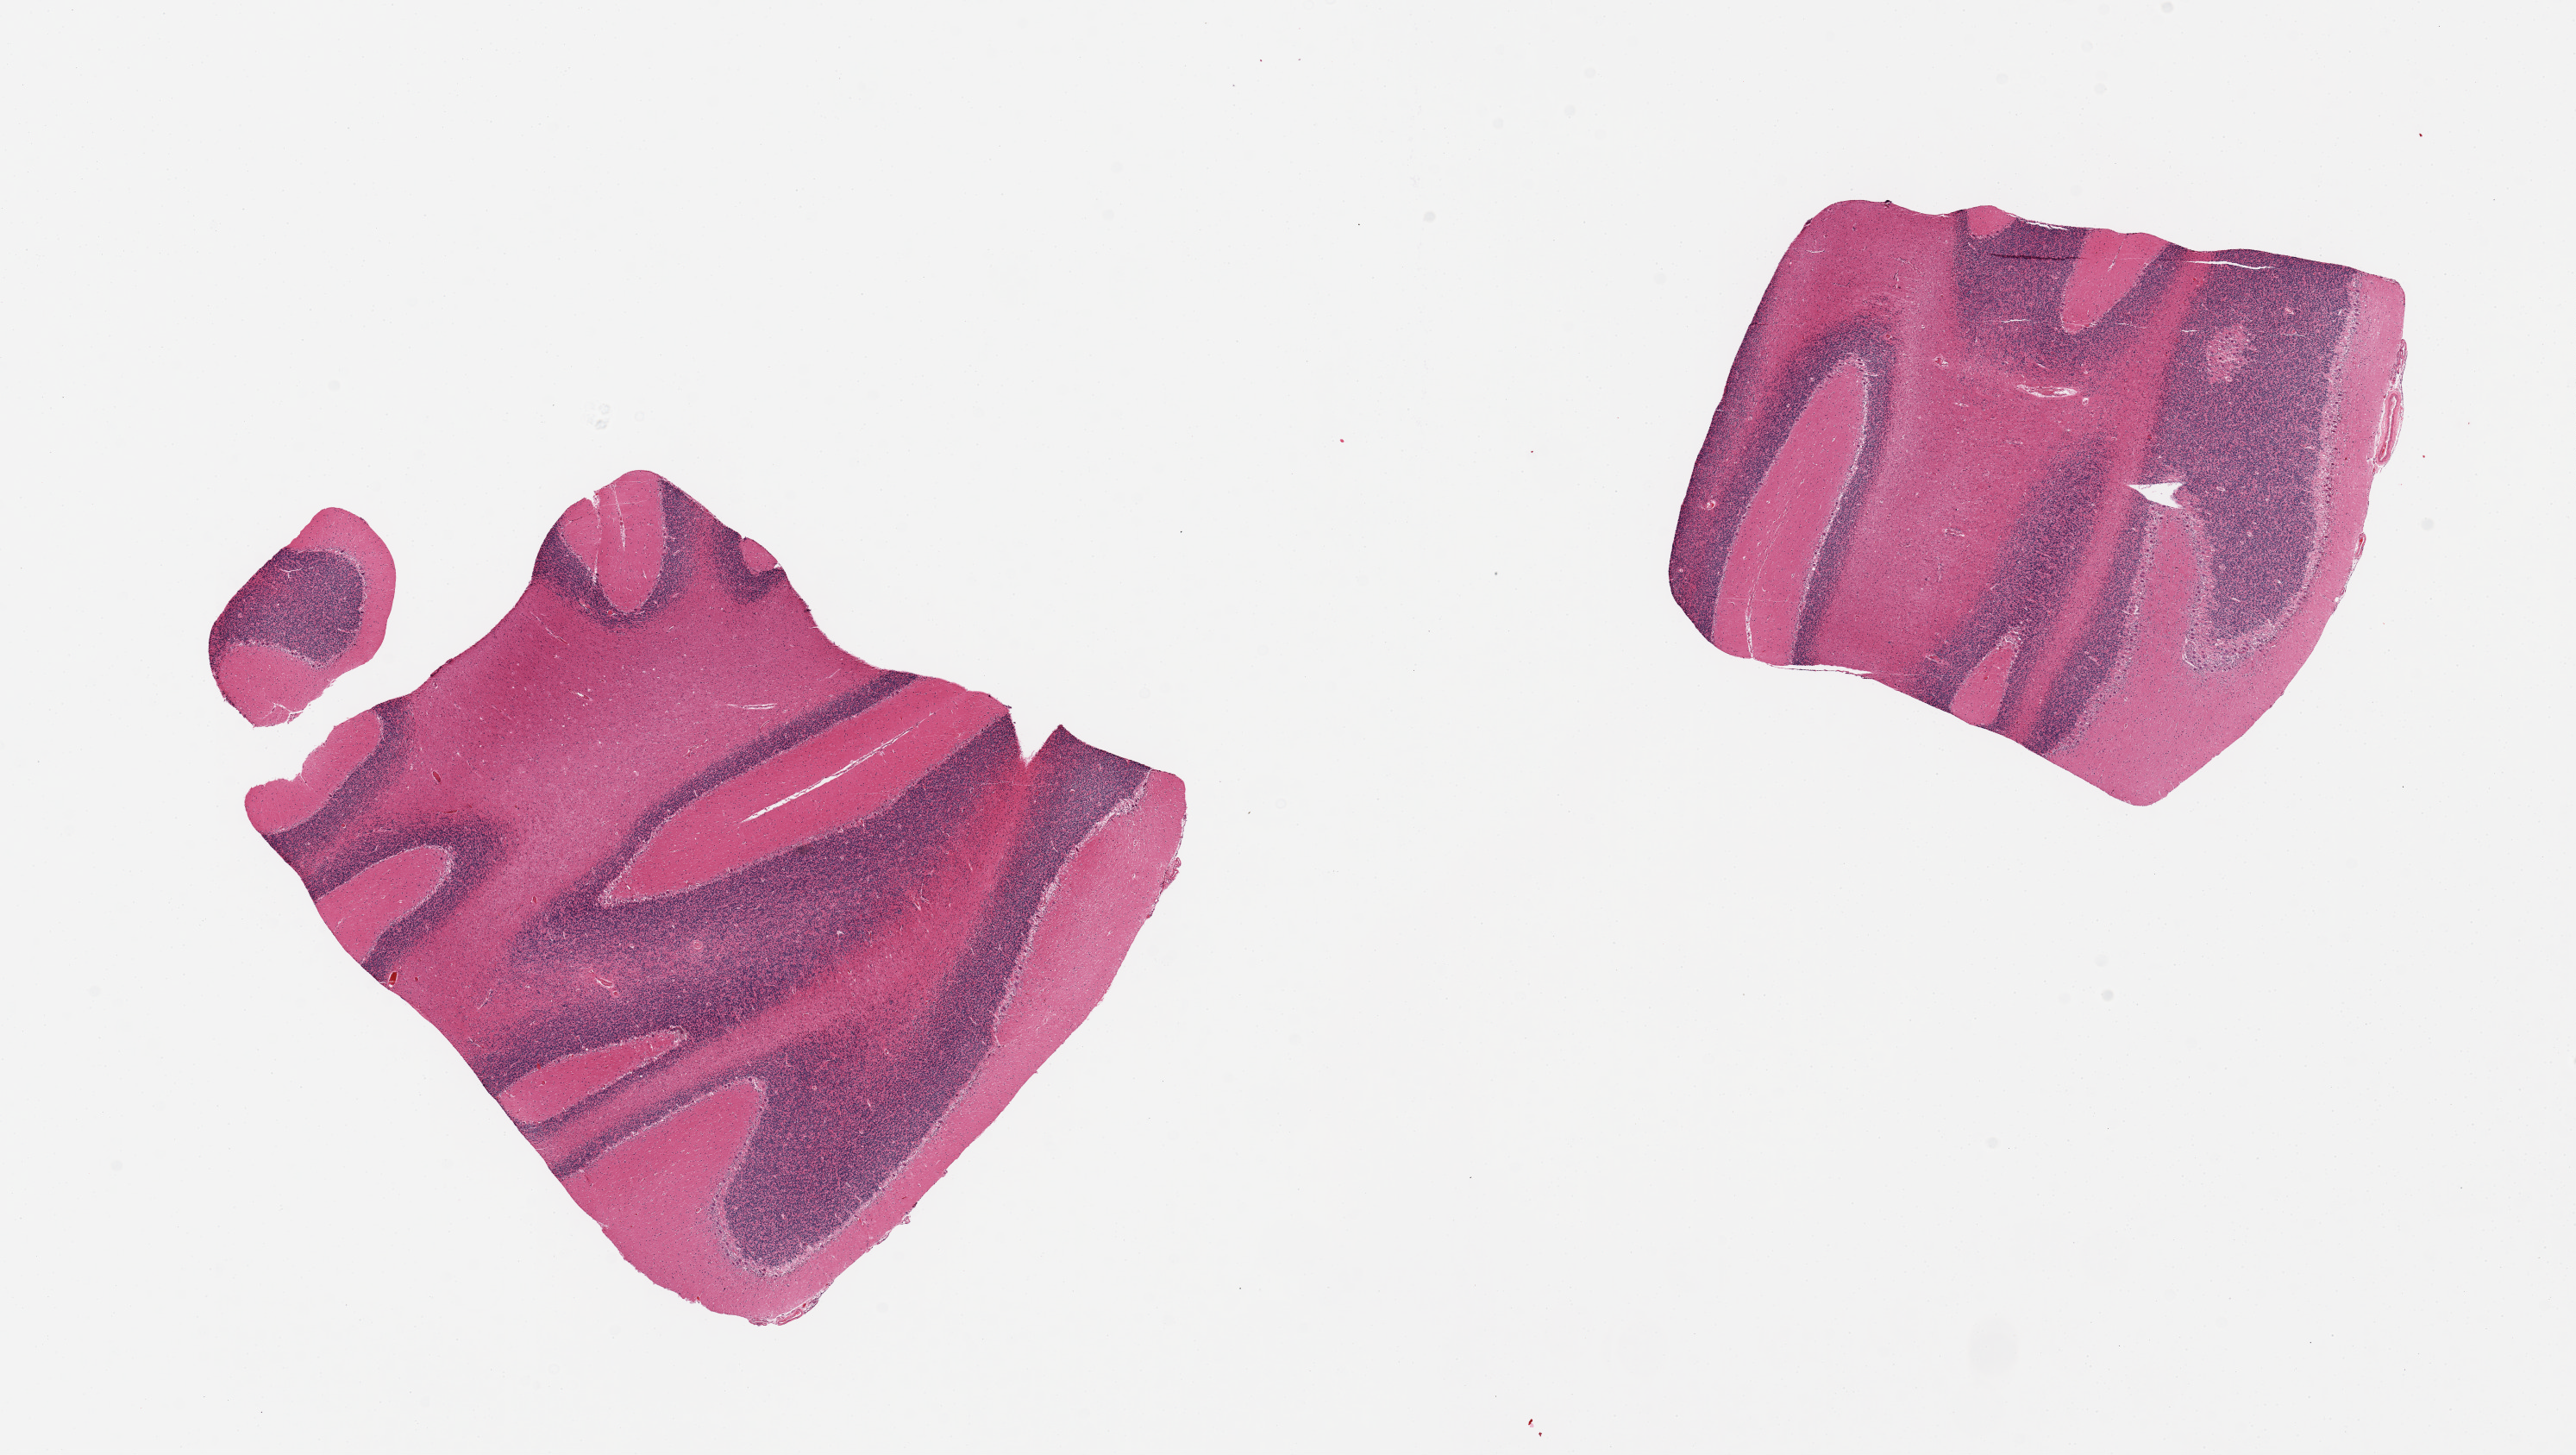
Hematoxylin and eosin (H&E) whole-slide image, shown as a low-resolution overview of the whole scanned area (about 23.6 x 13.3 mm); PAXgene-fixed paraffin-embedded (PFPE) section; sampled site (target tissue): cerebellum; donor tissue sample. Donor sex: male.
Pathologist's review note for this sample: 2 pieces.